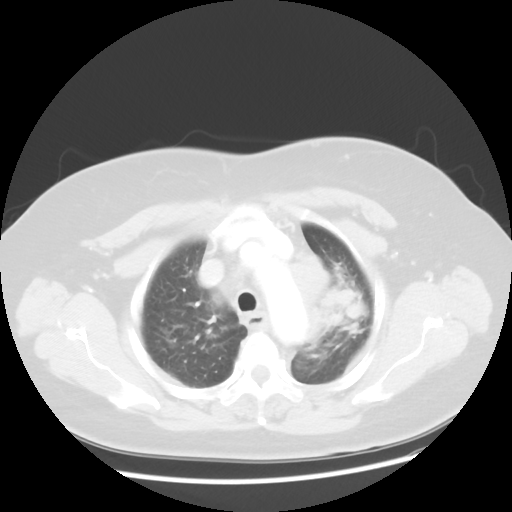
Chest CT, one axial slice. Position 38 of 49 along the scan axis. Reconstruction kernel STANDARD. 120 kVp. Lung window (W 1500 / L -600 HU). 512 × 512 image matrix, field of view 374 × 374 mm. Patient: female, 58 years. From the clinical record (not read from this slice): clinical TNM (as recorded): T4 N3 M0; histopathological grade: G3.
Outlined on this slice (rectangle marked by the reading radiologist):
- lung tumour (recorded histology: small cell carcinoma): bounding box (x1, y1, x2, y2) in pixels: (290, 247, 371, 342)